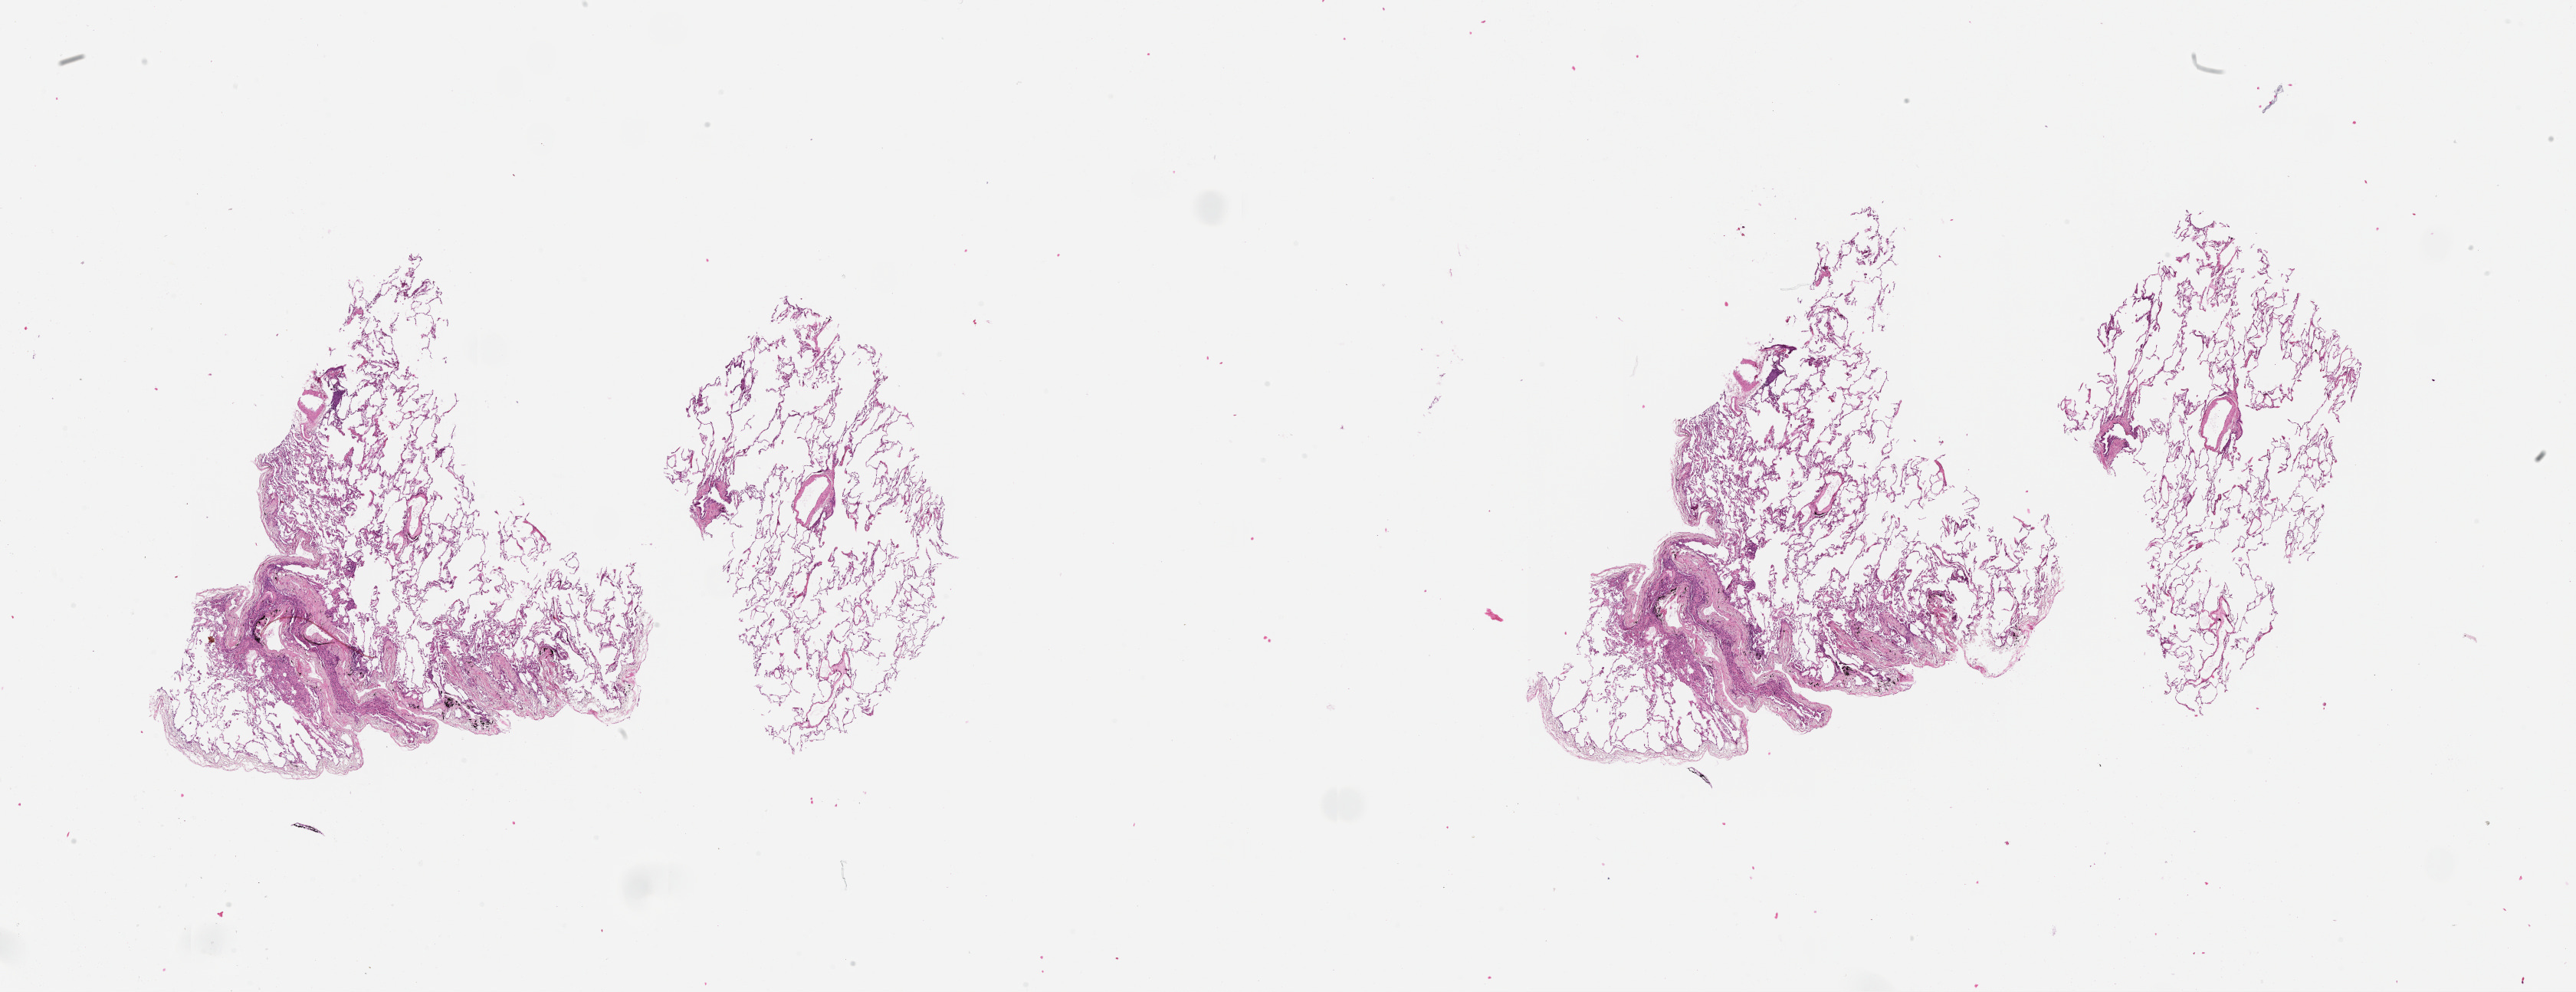
Whole-slide histology image, H&E-stained — a low-resolution overview of the entire scanned area, about 27.1 x 10.4 mm (acquisition: 20x scan); normal (non-tumour) tissue sample, sampled site: lung. 60-year-old male patient.
This section: normal (non-tumour) tissue from the same patient. Patient diagnosis: Adenocarcinoma, NOS.